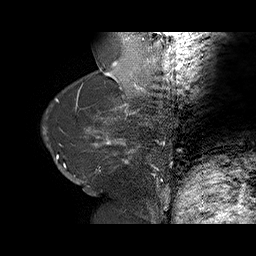
Breast MRI (dynamic contrast-enhanced), one sagittal slice; position 20 of 75 along the scan axis; dynamic contrast-enhanced series, time point 2 of 6 at this slice position (early post-contrast); 1.5 T; TE 4.5 ms, TR 32.4 ms; 3 mm slice thickness; 256 × 256 image matrix, field of view 180 × 180 mm. Female patient. From the clinical record (not read from this slice): setting: breast cancer imaged before/during neoadjuvant chemotherapy; receptor status: HR-positive, HER2-negative.
Outlined on this slice (semi-automatic segmentation, software-assisted and operator-edited):
- analysis volume of interest (the breast-tissue region the enhancement analysis was run in; not a lesion): box from (x=58, y=134) to (x=166, y=191) px
- tumour enhancement mask (voxels above the 100 % enhancement threshold inside the analysis volume of interest): (x=94, y=136)–(x=159, y=186)